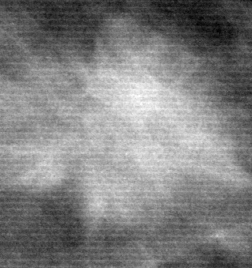
Crop from a digitized film mammogram around one marked abnormality; left breast; CC view.
- Marked abnormality: mass, shape round, margins spiculated; BI-RADS assessment category 5; pathology (as recorded): malignant.